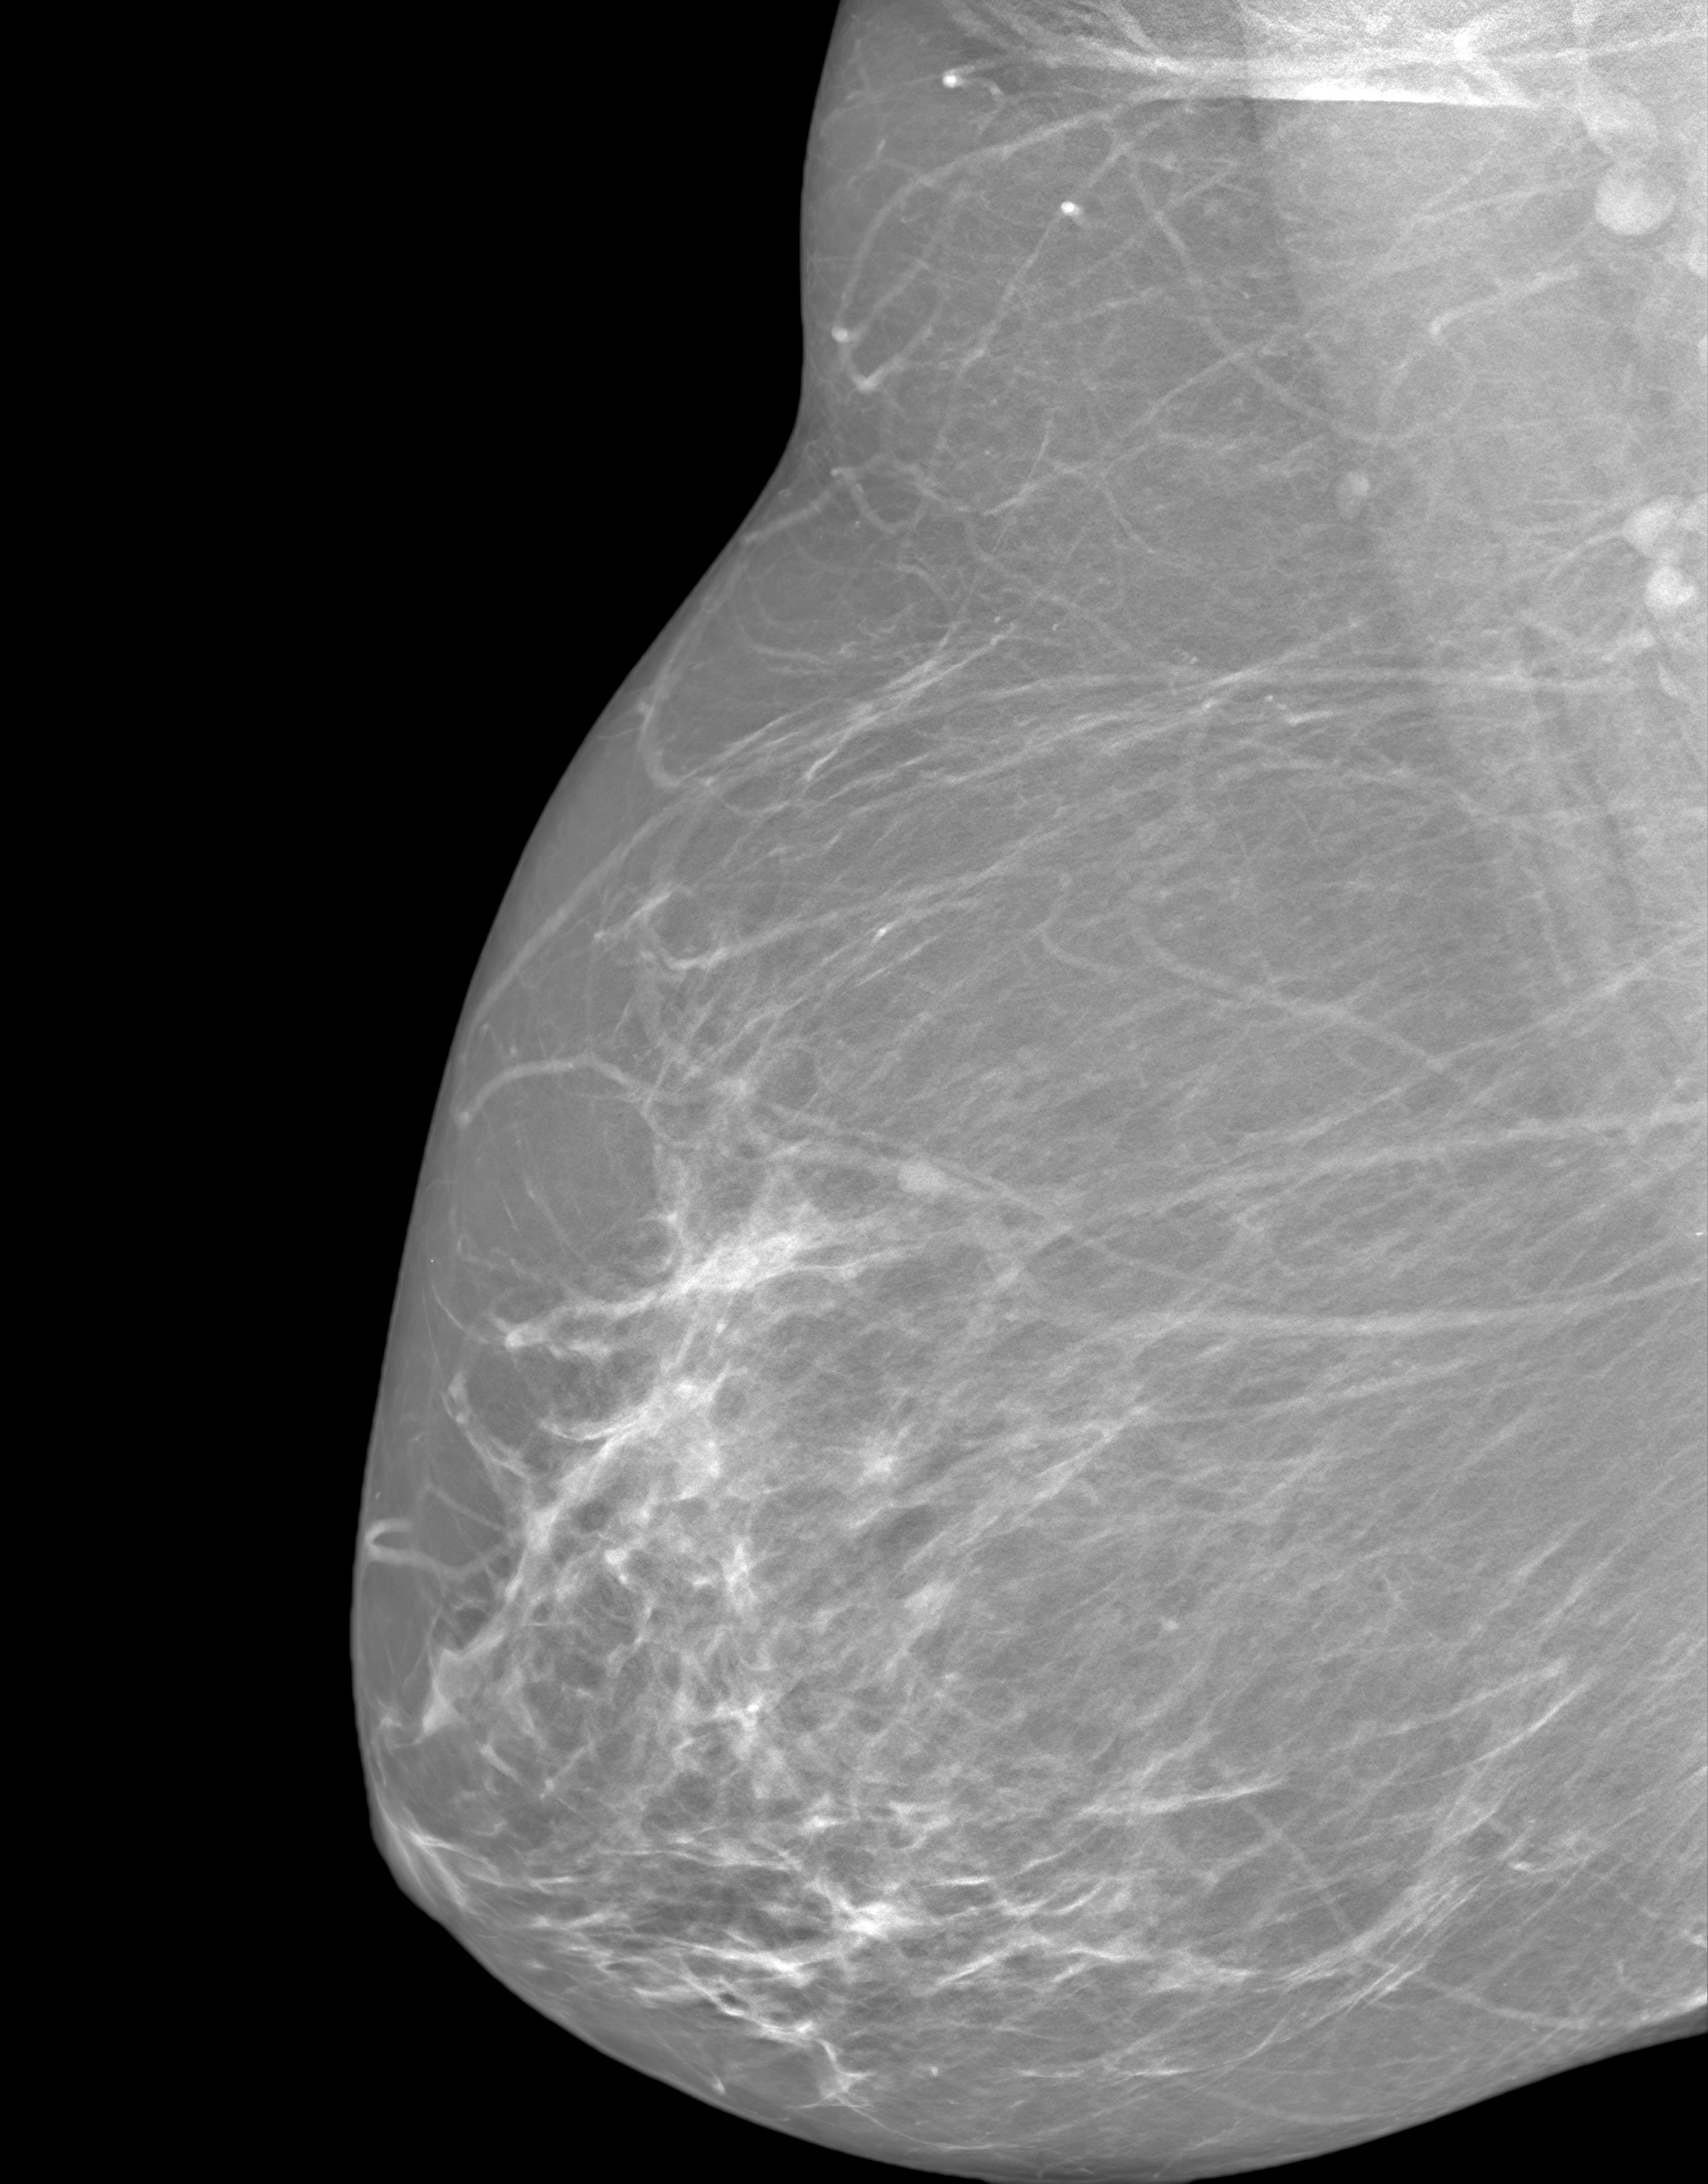
Screening examination; system: SenoIris_1SP2(440). Patient aged 59 years (female).
Image type: synthesized 2-D view from tomosynthesis. Breast: right. Projection: medio-lateral oblique projection.